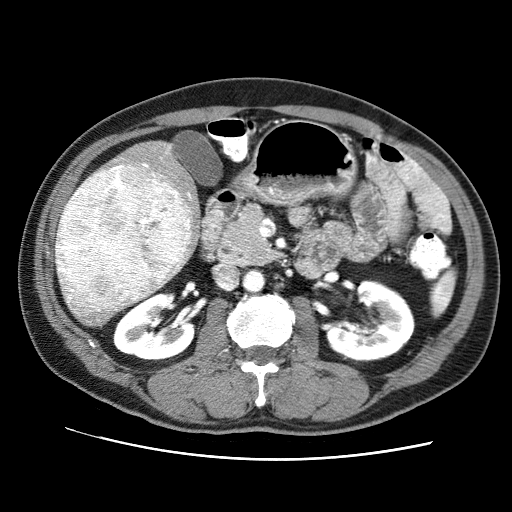
Contrast-enhanced abdominal CT (liver protocol), one axial slice. Position 30 of 71 along the scan axis. 120 kVp. Soft-tissue window (W 400 / L 40 HU). 512 × 512 image matrix, field of view 360 × 360 mm. From the clinical record (not read from this slice): diagnosis: hepatocellular carcinoma (patient treated with transarterial chemoembolisation; whether this scan precedes or follows treatment is not stated here); TNM stage (as recorded): Stage-II.
Structures marked on this image (semi-automatically segmented with operator editing):
- liver parenchyma outside the tumour (the mass and vessels are separate outlines, so this box may not span the whole liver): box from (x=73, y=139) to (x=200, y=299) px
- mass: (x=54, y=162)–(x=192, y=327)
- liver vessels: (x=144, y=146)–(x=191, y=278)